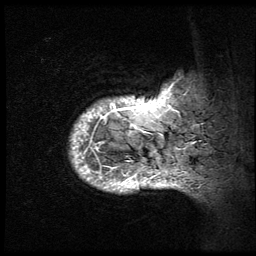
Breast MRI (dynamic contrast-enhanced), one sagittal slice; position 7 of 64 along the scan axis; 3 images stored at this slice position (order not interpretable as contrast timing); 1.5 T; TE 4.2 ms, TR 9 ms; 2.5 mm slice thickness; 256 × 256 image matrix, field of view 180 × 180 mm. Female patient, age 50 years. Case-level facts recorded for this patient, not image findings: setting: breast cancer imaged before/during neoadjuvant chemotherapy; receptor status: triple-negative.
Annotated regions visible in this slice (semi-automatically segmented with operator editing):
- analysis volume of interest (the breast-tissue region the enhancement analysis was run in; not a lesion): bounding box [x1, y1, x2, y2] px = [65, 69, 194, 208]
- tumour enhancement mask (voxels above the 140 % enhancement threshold inside the analysis volume of interest): [71, 79, 191, 193]